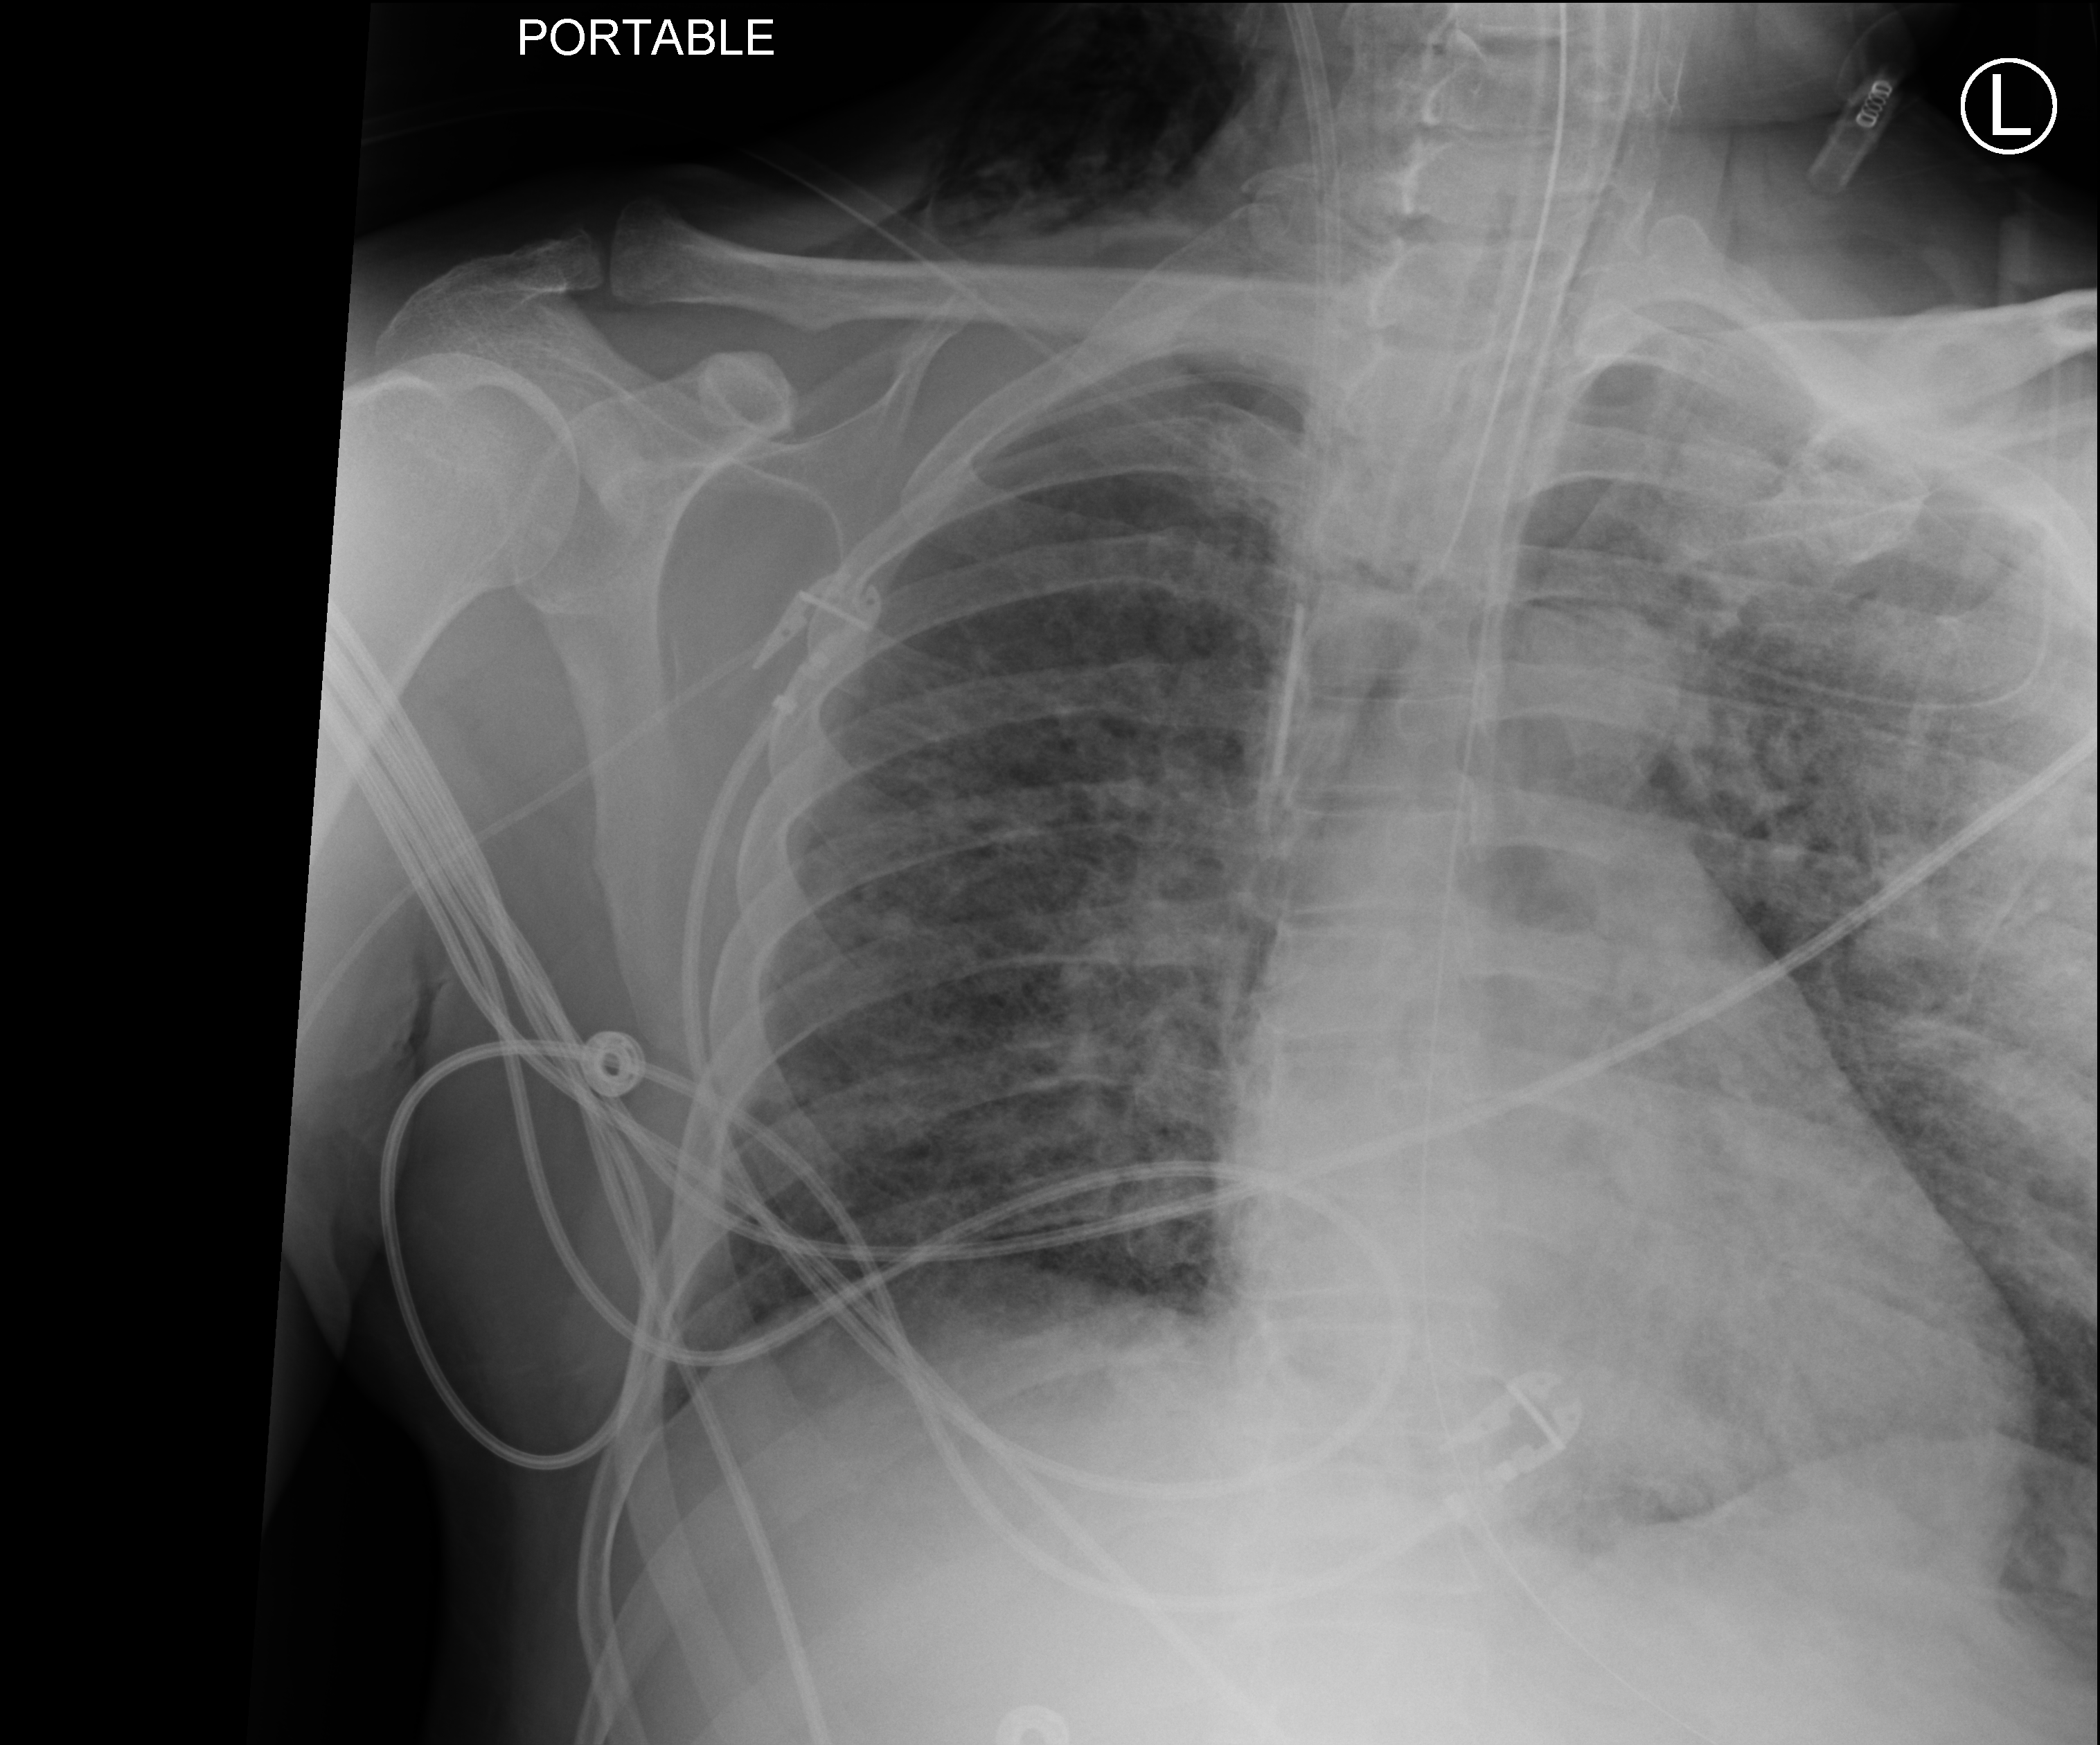
Portable chest radiograph; anteroposterior (AP) projection. Patient hospitalised with COVID-19; male, aged 18–59 years.
Admission-level facts for this patient (not findings on this image; timing relative to this image not recorded): mechanically ventilated during this hospital stay: yes.